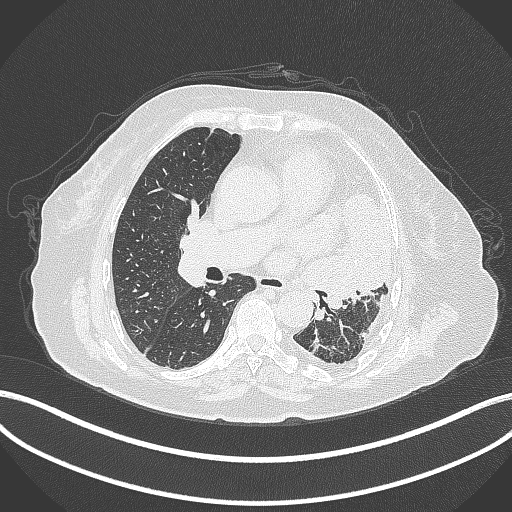
Chest CT, one axial slice; slice 199 of 399 in the series (ordered by position); reconstruction kernel B70f; lung window (W 1500 / L -600 HU); 1 mm slice thickness; 512 × 512 image matrix, field of view 400 × 400 mm. Patient: female, 75 years. Case-level facts recorded for this patient, not image findings: clinical TNM (as recorded): T3 N3 M1.
Structures marked on this image (bounding box drawn by a radiologist):
- lung tumour (recorded histology: adenocarcinoma): bounding box (x1, y1, x2, y2) in pixels: (293, 189, 399, 314)